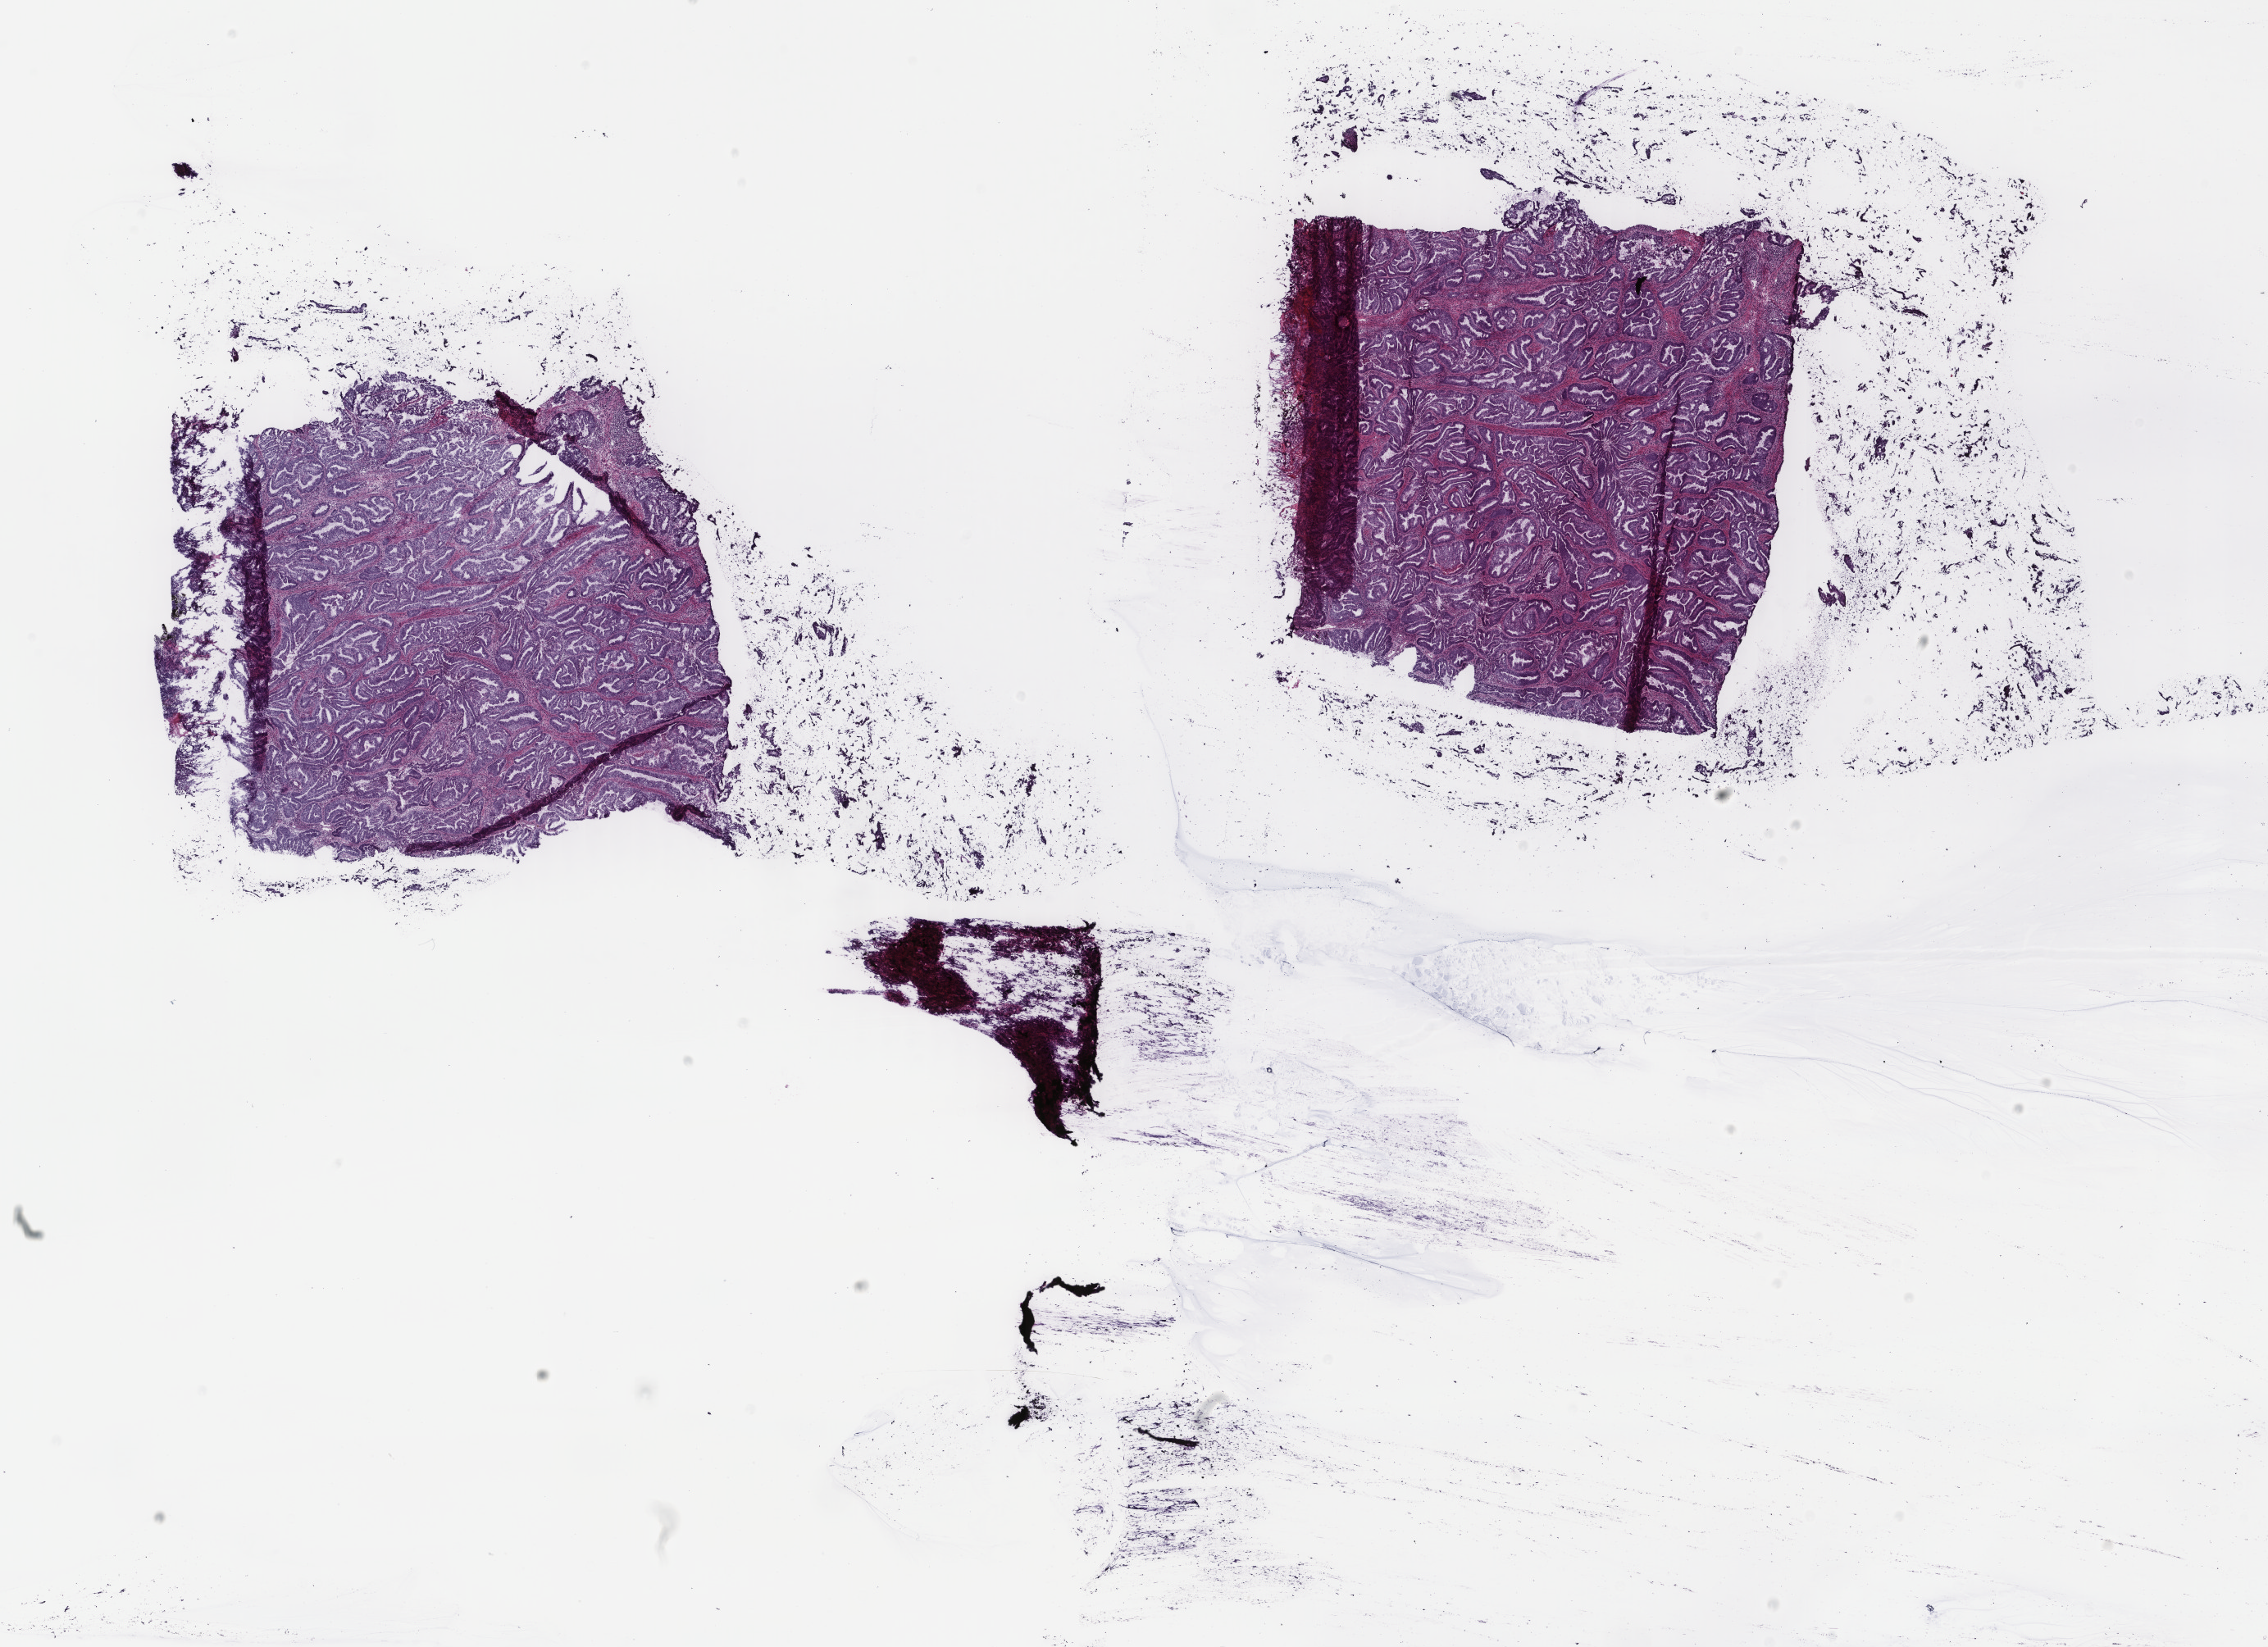
H&E-stained whole-slide image — shown as a low-resolution overview of the whole scanned area (about 22.0 x 15.9 mm), frozen section from the top of the tissue portion, sample: primary tumour, uterus. Female patient; age at initial diagnosis 52 years. Histologic grade: G2 (moderately differentiated). Slide review estimates, as recorded: tumour cells 100%, tumour nuclei 85%, normal cells 0%, stromal cells 0%, necrosis 0%. Inflammatory infiltration, as recorded: lymphocyte infiltration 0%, monocyte infiltration 0%, neutrophil infiltration 0%.
• lymph nodes positive (case pathology): 0 of 23 examined
• pathologic diagnosis: Endometrioid adenocarcinoma, NOS (endometrium)
• FIGO stage: IB